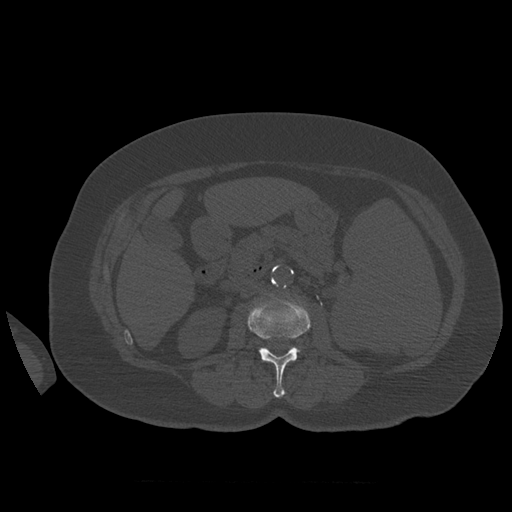
CT including the spine, one axial slice. Slice 250 of 399 in the series (ordered by position). Reconstruction kernel STANDARD. 120 kVp. Bone window (W 1800 / L 400 HU). 1.25 mm slice thickness. 512 × 512 image matrix. Patient age 81 years. Case-level facts recorded for this patient, not image findings: primary cancer: renal.
Outlined on this slice (semi-automatically segmented with operator editing):
- L2 vertebra: bounding box [x1, y1, x2, y2] px = [248, 298, 311, 398]